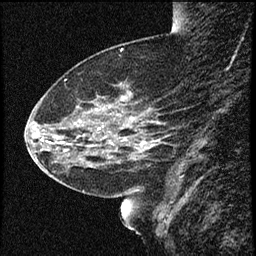
Breast MRI (dynamic contrast-enhanced), one sagittal slice; slice 19 of 60 in the series (ordered by position); dynamic contrast-enhanced study with each time point stored as its own series, time point 2 of 4 at this slice position (early post-contrast, ordered by acquisition time); 1.5 T; TE 4.2 ms, TR 16.7 ms; 256 × 256 image matrix, field of view 200 × 200 mm. Patient: female, 52 years. Case-level facts recorded for this patient, not image findings: setting: breast cancer imaged before/during neoadjuvant chemotherapy; receptor status: HER2-positive.
Structures marked on this image (semi-automatic segmentation, software-assisted and operator-edited):
- analysis volume of interest (the breast-tissue region the enhancement analysis was run in; not a lesion): box from (x=37, y=79) to (x=165, y=181) px
- tumour enhancement mask (voxels above the 100 % enhancement threshold inside the analysis volume of interest): (x=143, y=143)–(x=147, y=149)